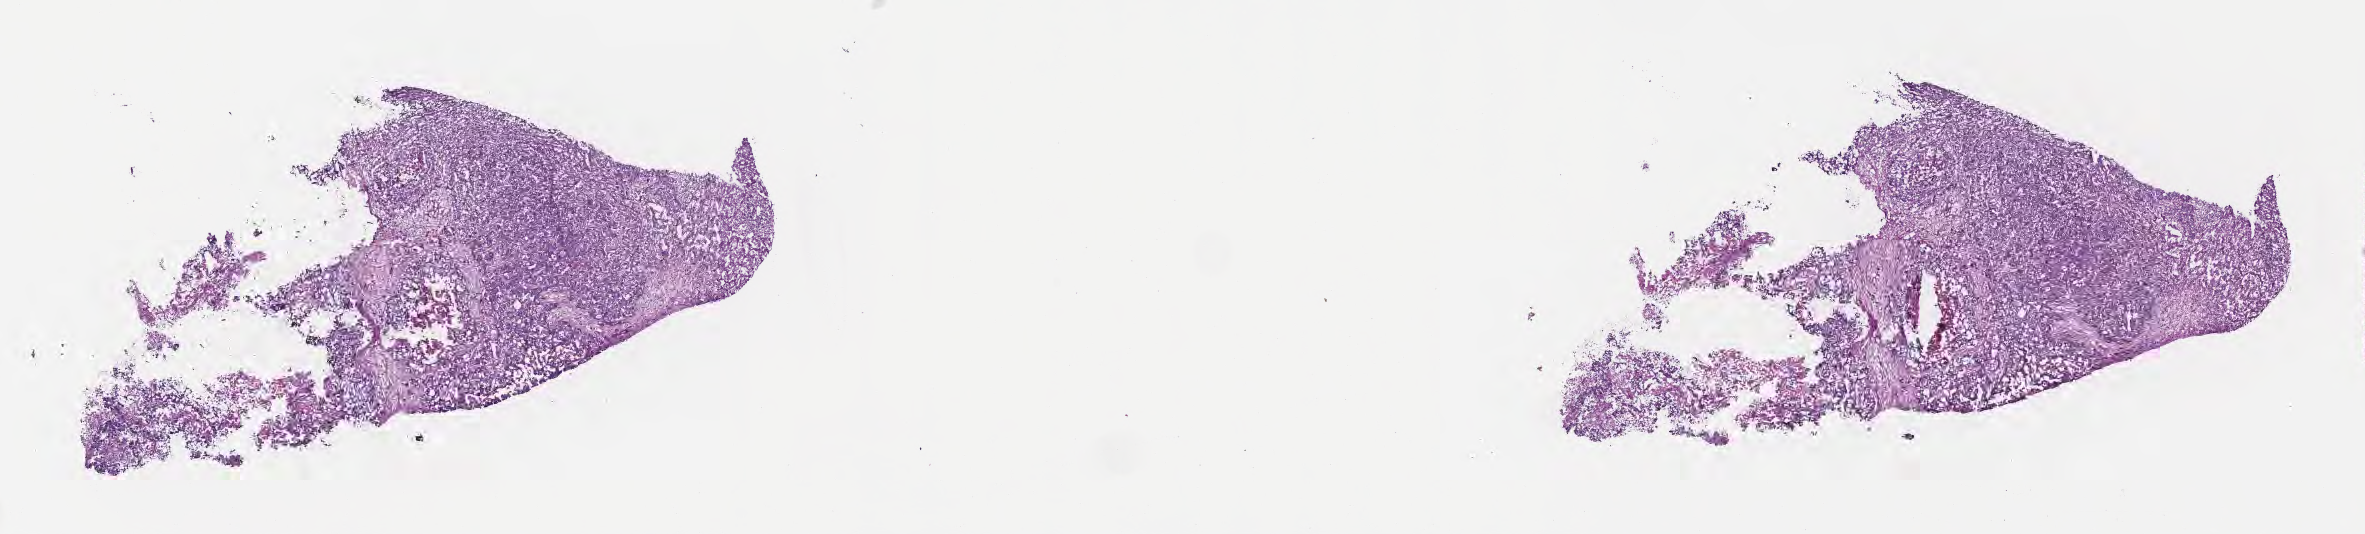
Haematoxylin and eosin whole-slide image, low-resolution overview of the scanned area, about 19.1 x 4.3 mm; frozen section; metastatic tumor tissue, resected from liver. Male, age 69 years at initial diagnosis.
Patient diagnosis (primary): Adenocarcinoma, NOS.